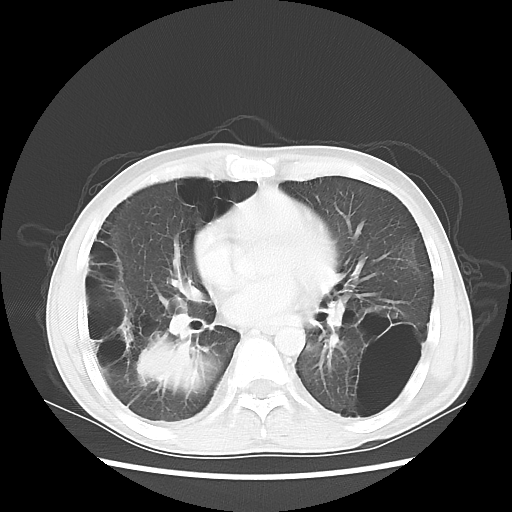
Chest CT, one axial slice; position 26 of 57 along the scan axis; lung window (W 1500 / L -600 HU); 5 mm slice thickness; 512 × 512 image matrix, field of view 351 × 351 mm. Male patient, age 41 years. From the clinical record (not read from this slice): clinical TNM (as recorded): T4 N0 M1a.
Structures marked on this image (rectangle marked by the reading radiologist):
- lung tumour (recorded histology: large cell carcinoma): box from (x=137, y=332) to (x=215, y=409) px